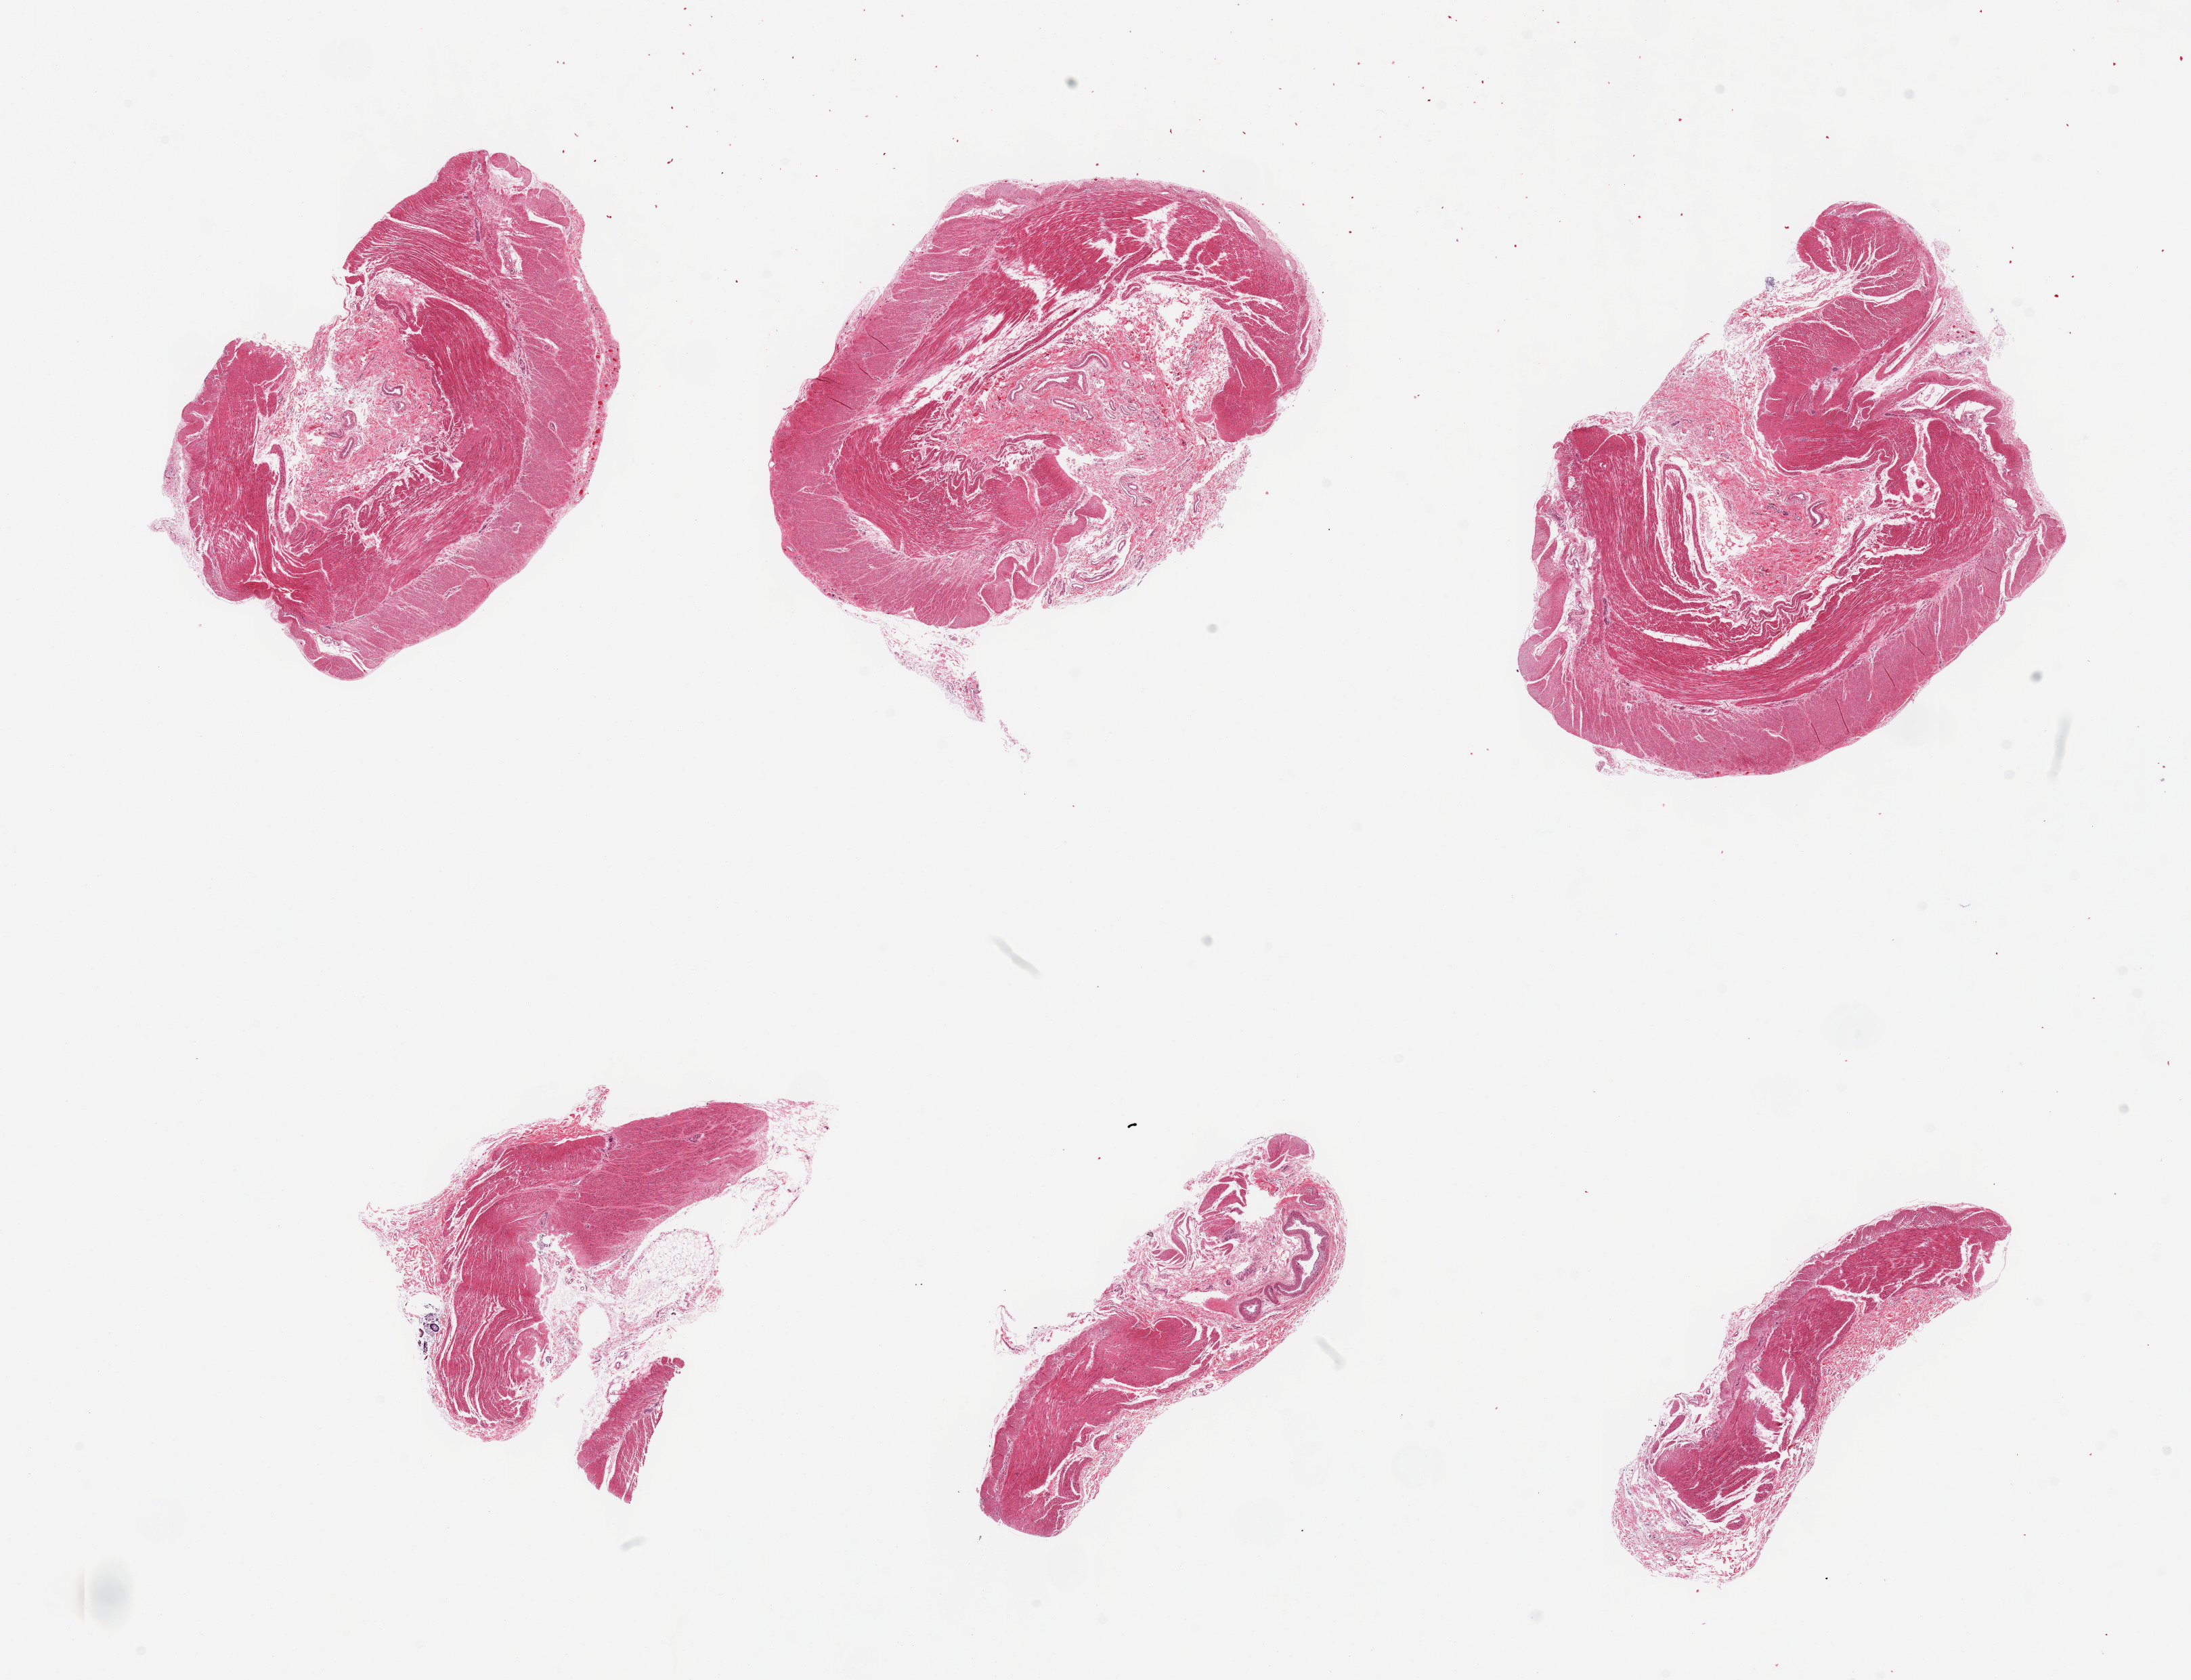
Haematoxylin and eosin whole-slide image — low-resolution overview of the scanned area, about 25.6 x 19.6 mm (acquisition: 20x scan); PAXgene-fixed paraffin-embedded (PFPE) section; section of transverse colon (target tissue); donor tissue sample. Donor sex: female.
Review note (as recorded): 6 pieces; no mucosa. only muscularis and submucosa.